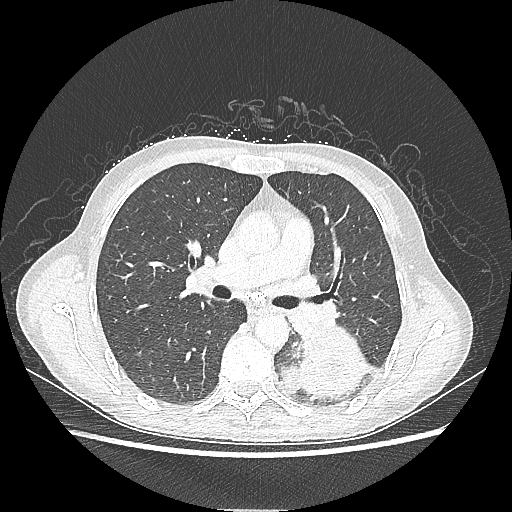
Chest CT, one axial slice. Slice 129 of 220 in the series (ordered by position). 80 kVp. Lung window (W 1500 / L -600 HU). 512 × 512 image matrix. Patient: female, 53 years. From the clinical record (not read from this slice): clinical TNM (as recorded): T3 N0 M0.
Structures marked on this image (rectangle marked by the reading radiologist):
- lung tumour (recorded histology: adenocarcinoma): bounding box [x1, y1, x2, y2] px = [279, 333, 369, 405]